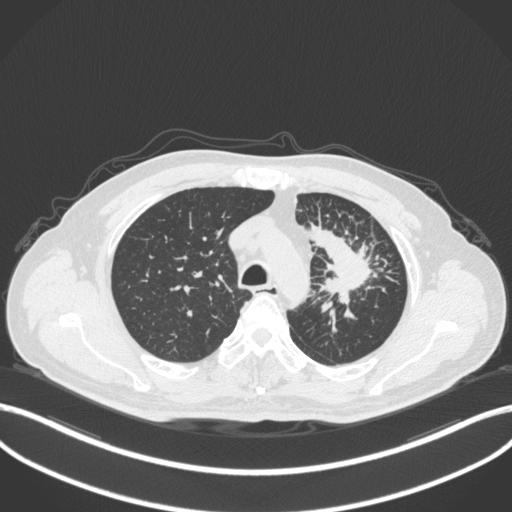
Chest CT, one axial slice; reconstruction kernel B31f; lung window (W 1500 / L -600 HU); 1 mm slice thickness; 512 × 512 image matrix, field of view 400 × 400 mm. Patient: male, 69 years. From the clinical record (not read from this slice): clinical TNM (as recorded): T2a N2 M0; histopathological grade: G2-3.
Annotated regions visible in this slice (bounding box drawn by a radiologist):
- lung tumour (recorded histology: adenocarcinoma): box from (x=305, y=220) to (x=380, y=306) px